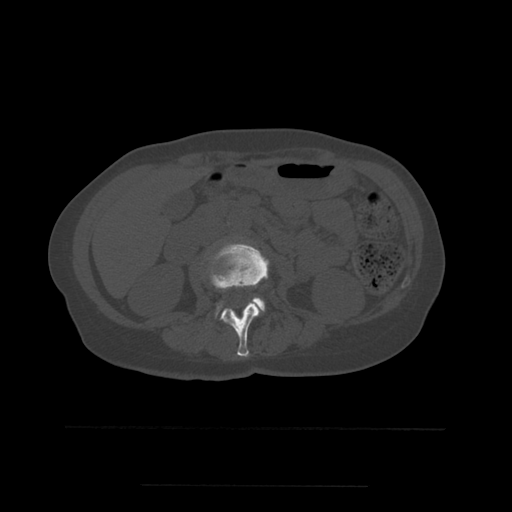
CT including the spine, one axial slice. Position 203 of 544 along the scan axis. Bone window (W 1800 / L 400 HU). 1.25 mm slice thickness. 512 × 512 image matrix, field of view 350 × 350 mm. Patient age 58 years. From the clinical record (not read from this slice): primary cancer: lung.
Annotated regions visible in this slice (semi-automatic segmentation, software-assisted and operator-edited):
- L2 vertebra: bounding box <210,243,269,357> (left, top, right, bottom; pixels)
- L3 vertebra: <216,298,265,316>